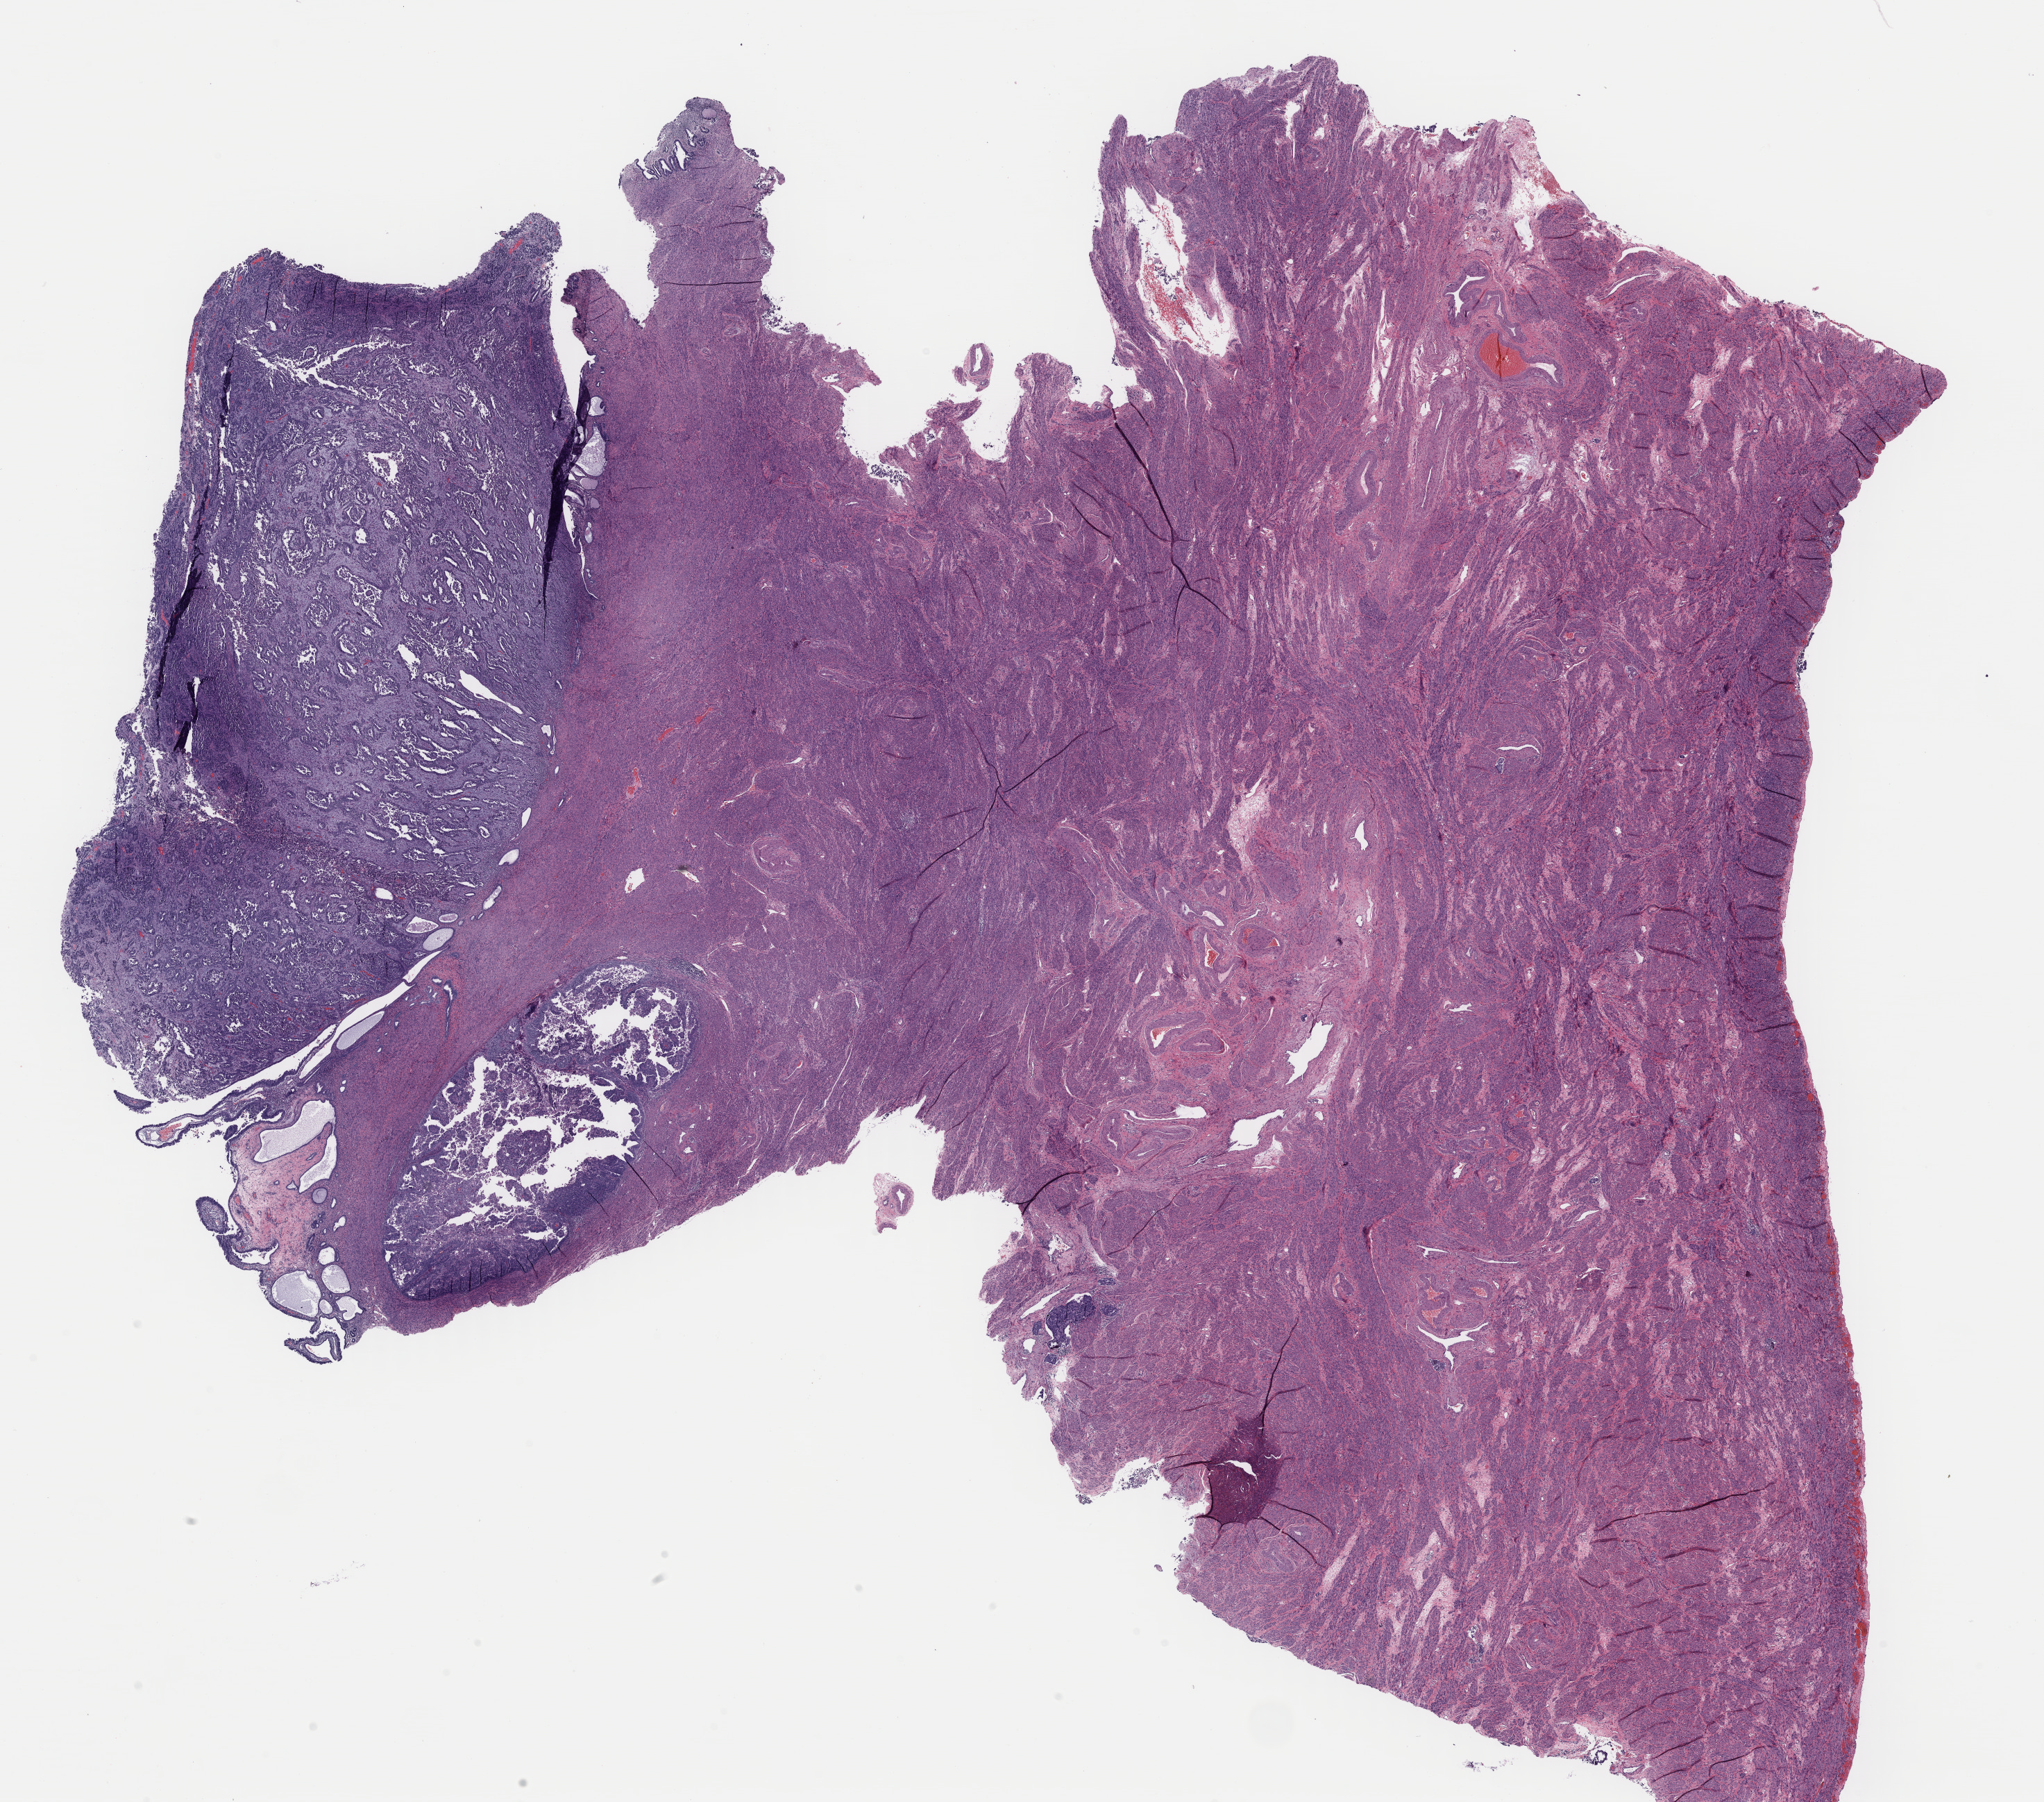
Whole-slide histology image, H&E-stained — low-resolution overview of the scanned area, about 23.2 x 20.5 mm (slide scanned at 40x). Formalin-fixed paraffin-embedded (FFPE) diagnostic section. Uterus, primary tumour sample. Patient: female, age at initial diagnosis 77 years.
- FIGO stage: IVB
- diagnosis: Mullerian mixed tumor (endometrium)